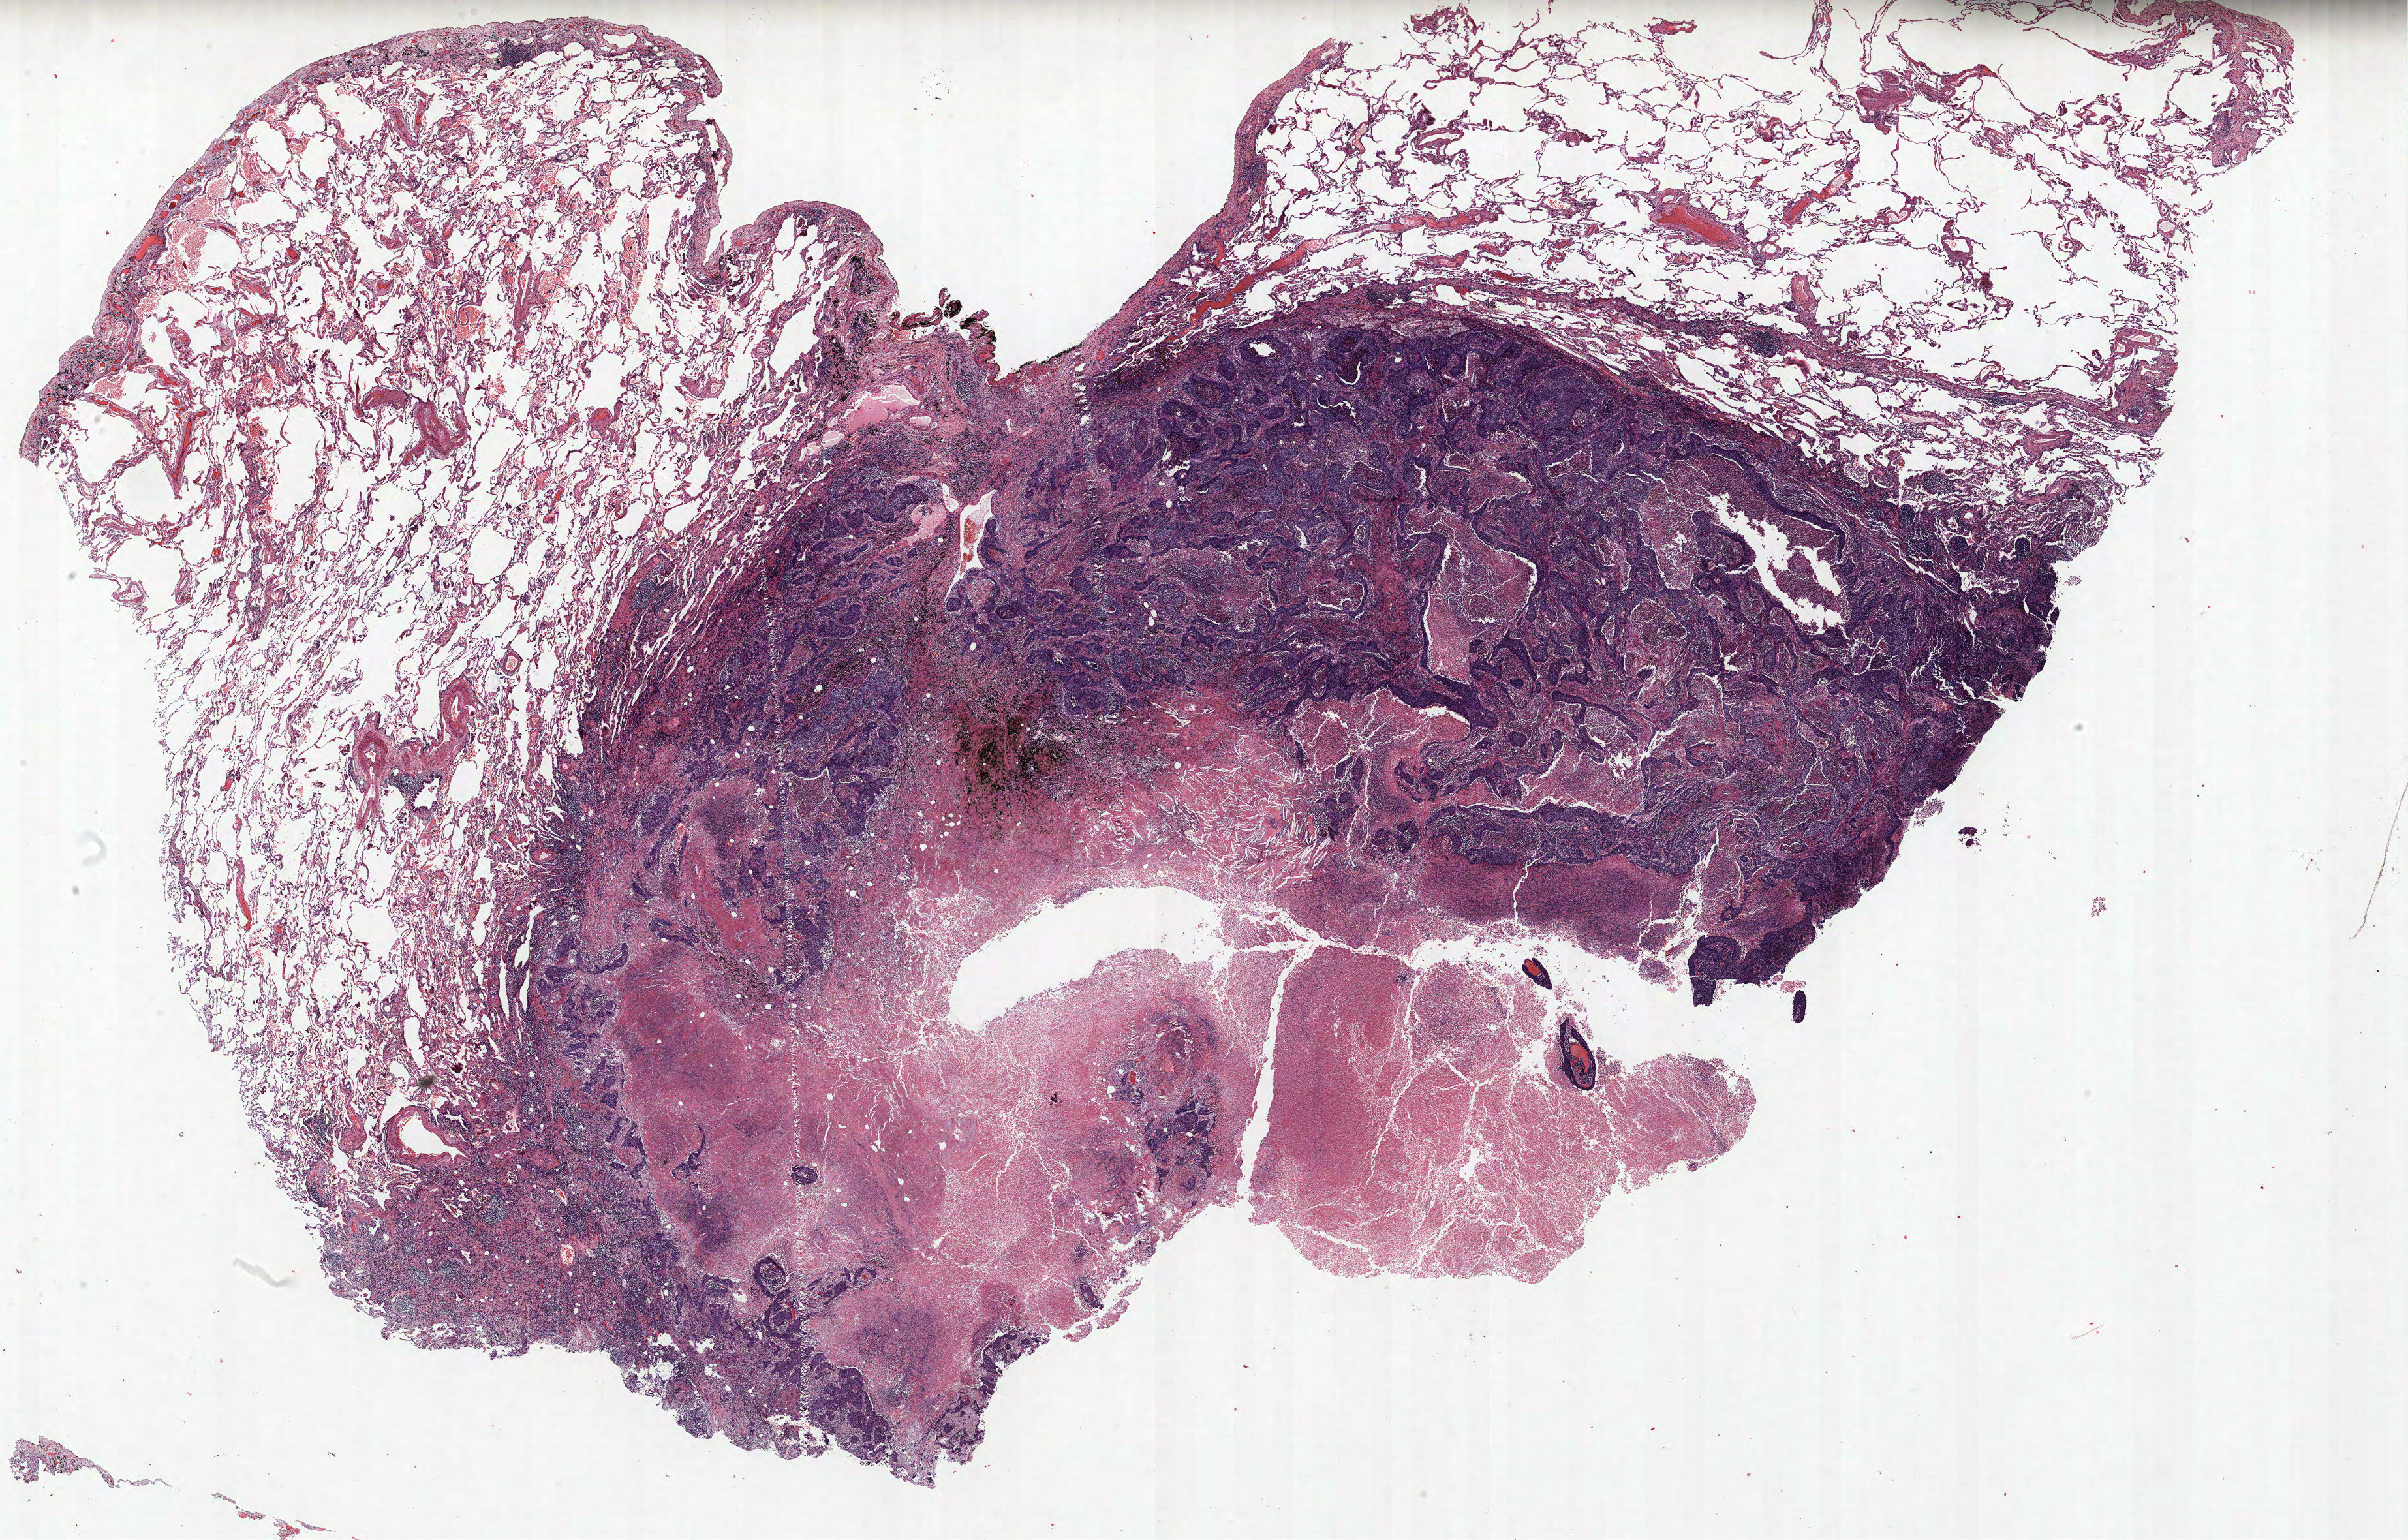
Whole-slide histology image, H&E-stained — low-resolution overview of the scanned area, about 29.5 x 18.9 mm. Formalin-fixed paraffin-embedded (FFPE) section. Lung. Male patient, aged 68 at enrolment. Former smoker at enrolment. Grade: moderately differentiated (G2).
Participant's lung-cancer diagnosis: Squamous cell carcinoma, NOS. Stage (AJCC 6th edition): IIB. Tumour size (pathology): 33 mm. Primary tumour location (clinical record): right upper lobe.